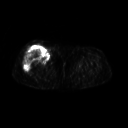
FDG PET of an extremity soft-tissue mass (from a PET/CT study), one axial slice. Position 243 of 311 along the scan axis. 3.27 mm slice thickness. 128 × 128 image matrix, field of view 500 × 500 mm. Female patient, age 57 years. Case-level facts recorded for this patient, not image findings: histological type: pleiomorphic undifferentiated sarcoma; grade: high; site of the primary tumour: right quadricep.
Outlined on this slice (expert contour drawn on MRI and transferred to this co-registered scan by the dataset authors):
- tumour plus oedema (research contour): box from (x=24, y=47) to (x=49, y=71) px
- tumour (research contour): (x=24, y=47)–(x=49, y=71)